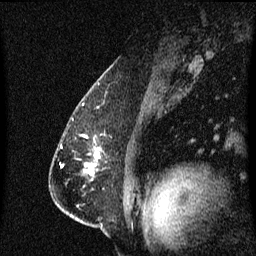
Breast MRI (dynamic contrast-enhanced), one sagittal slice; position 44 of 60 along the scan axis; dynamic contrast-enhanced series, image 2 of 3 at this slice position (ordered by acquisition); 1.5 T; TE 4.2 ms, TR 8.4 ms; 256 × 256 image matrix. Female patient, age 57 years. Case-level facts recorded for this patient, not image findings: setting: breast cancer imaged before/during neoadjuvant chemotherapy; receptor status: HR-positive, HER2-negative.
Structures marked on this image (semi-automatic segmentation, software-assisted and operator-edited):
- analysis volume of interest (the breast-tissue region the enhancement analysis was run in; not a lesion): bounding box (x1, y1, x2, y2) in pixels: (84, 140, 100, 175)
- tumour enhancement mask (voxels above the 70 % enhancement threshold inside the analysis volume of interest): (88, 152, 100, 171)